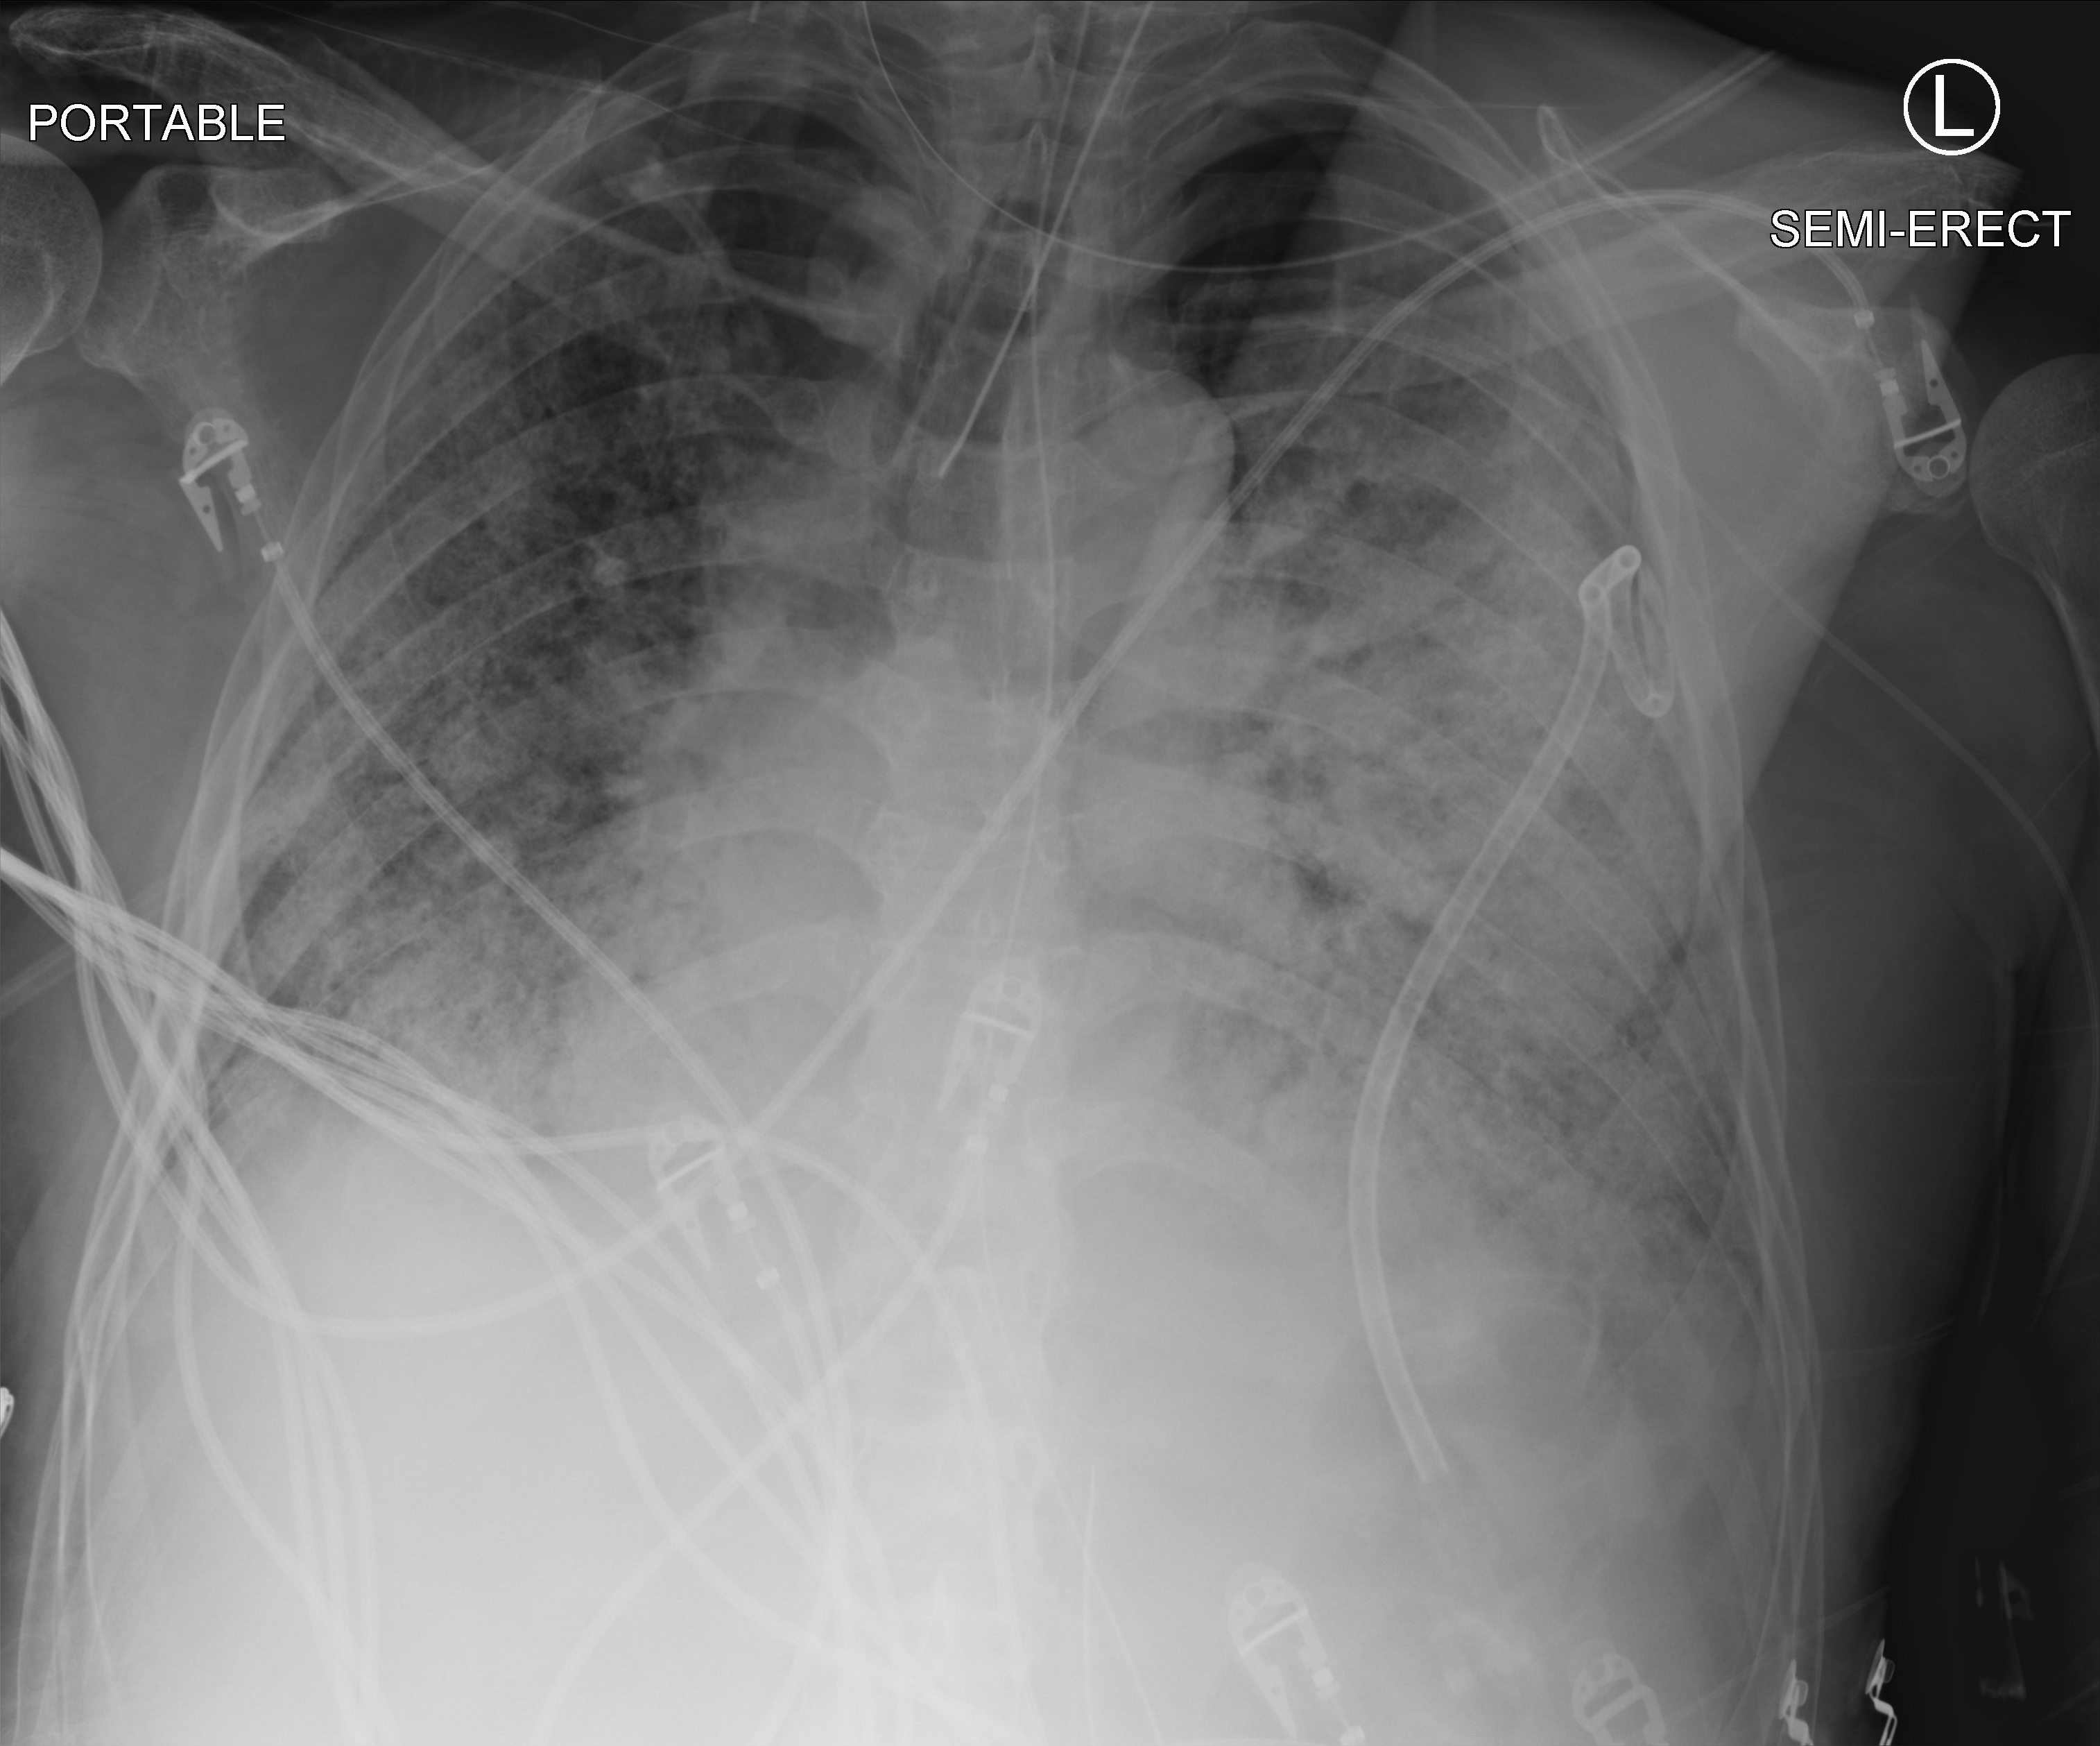
Portable chest radiograph, anteroposterior (AP) projection. Patient hospitalised with COVID-19; male, aged 60–74 years.
From the hospital-stay record, not from the radiograph (when in the stay this image was taken is not recorded):
- admitted to intensive care during this hospital stay: yes